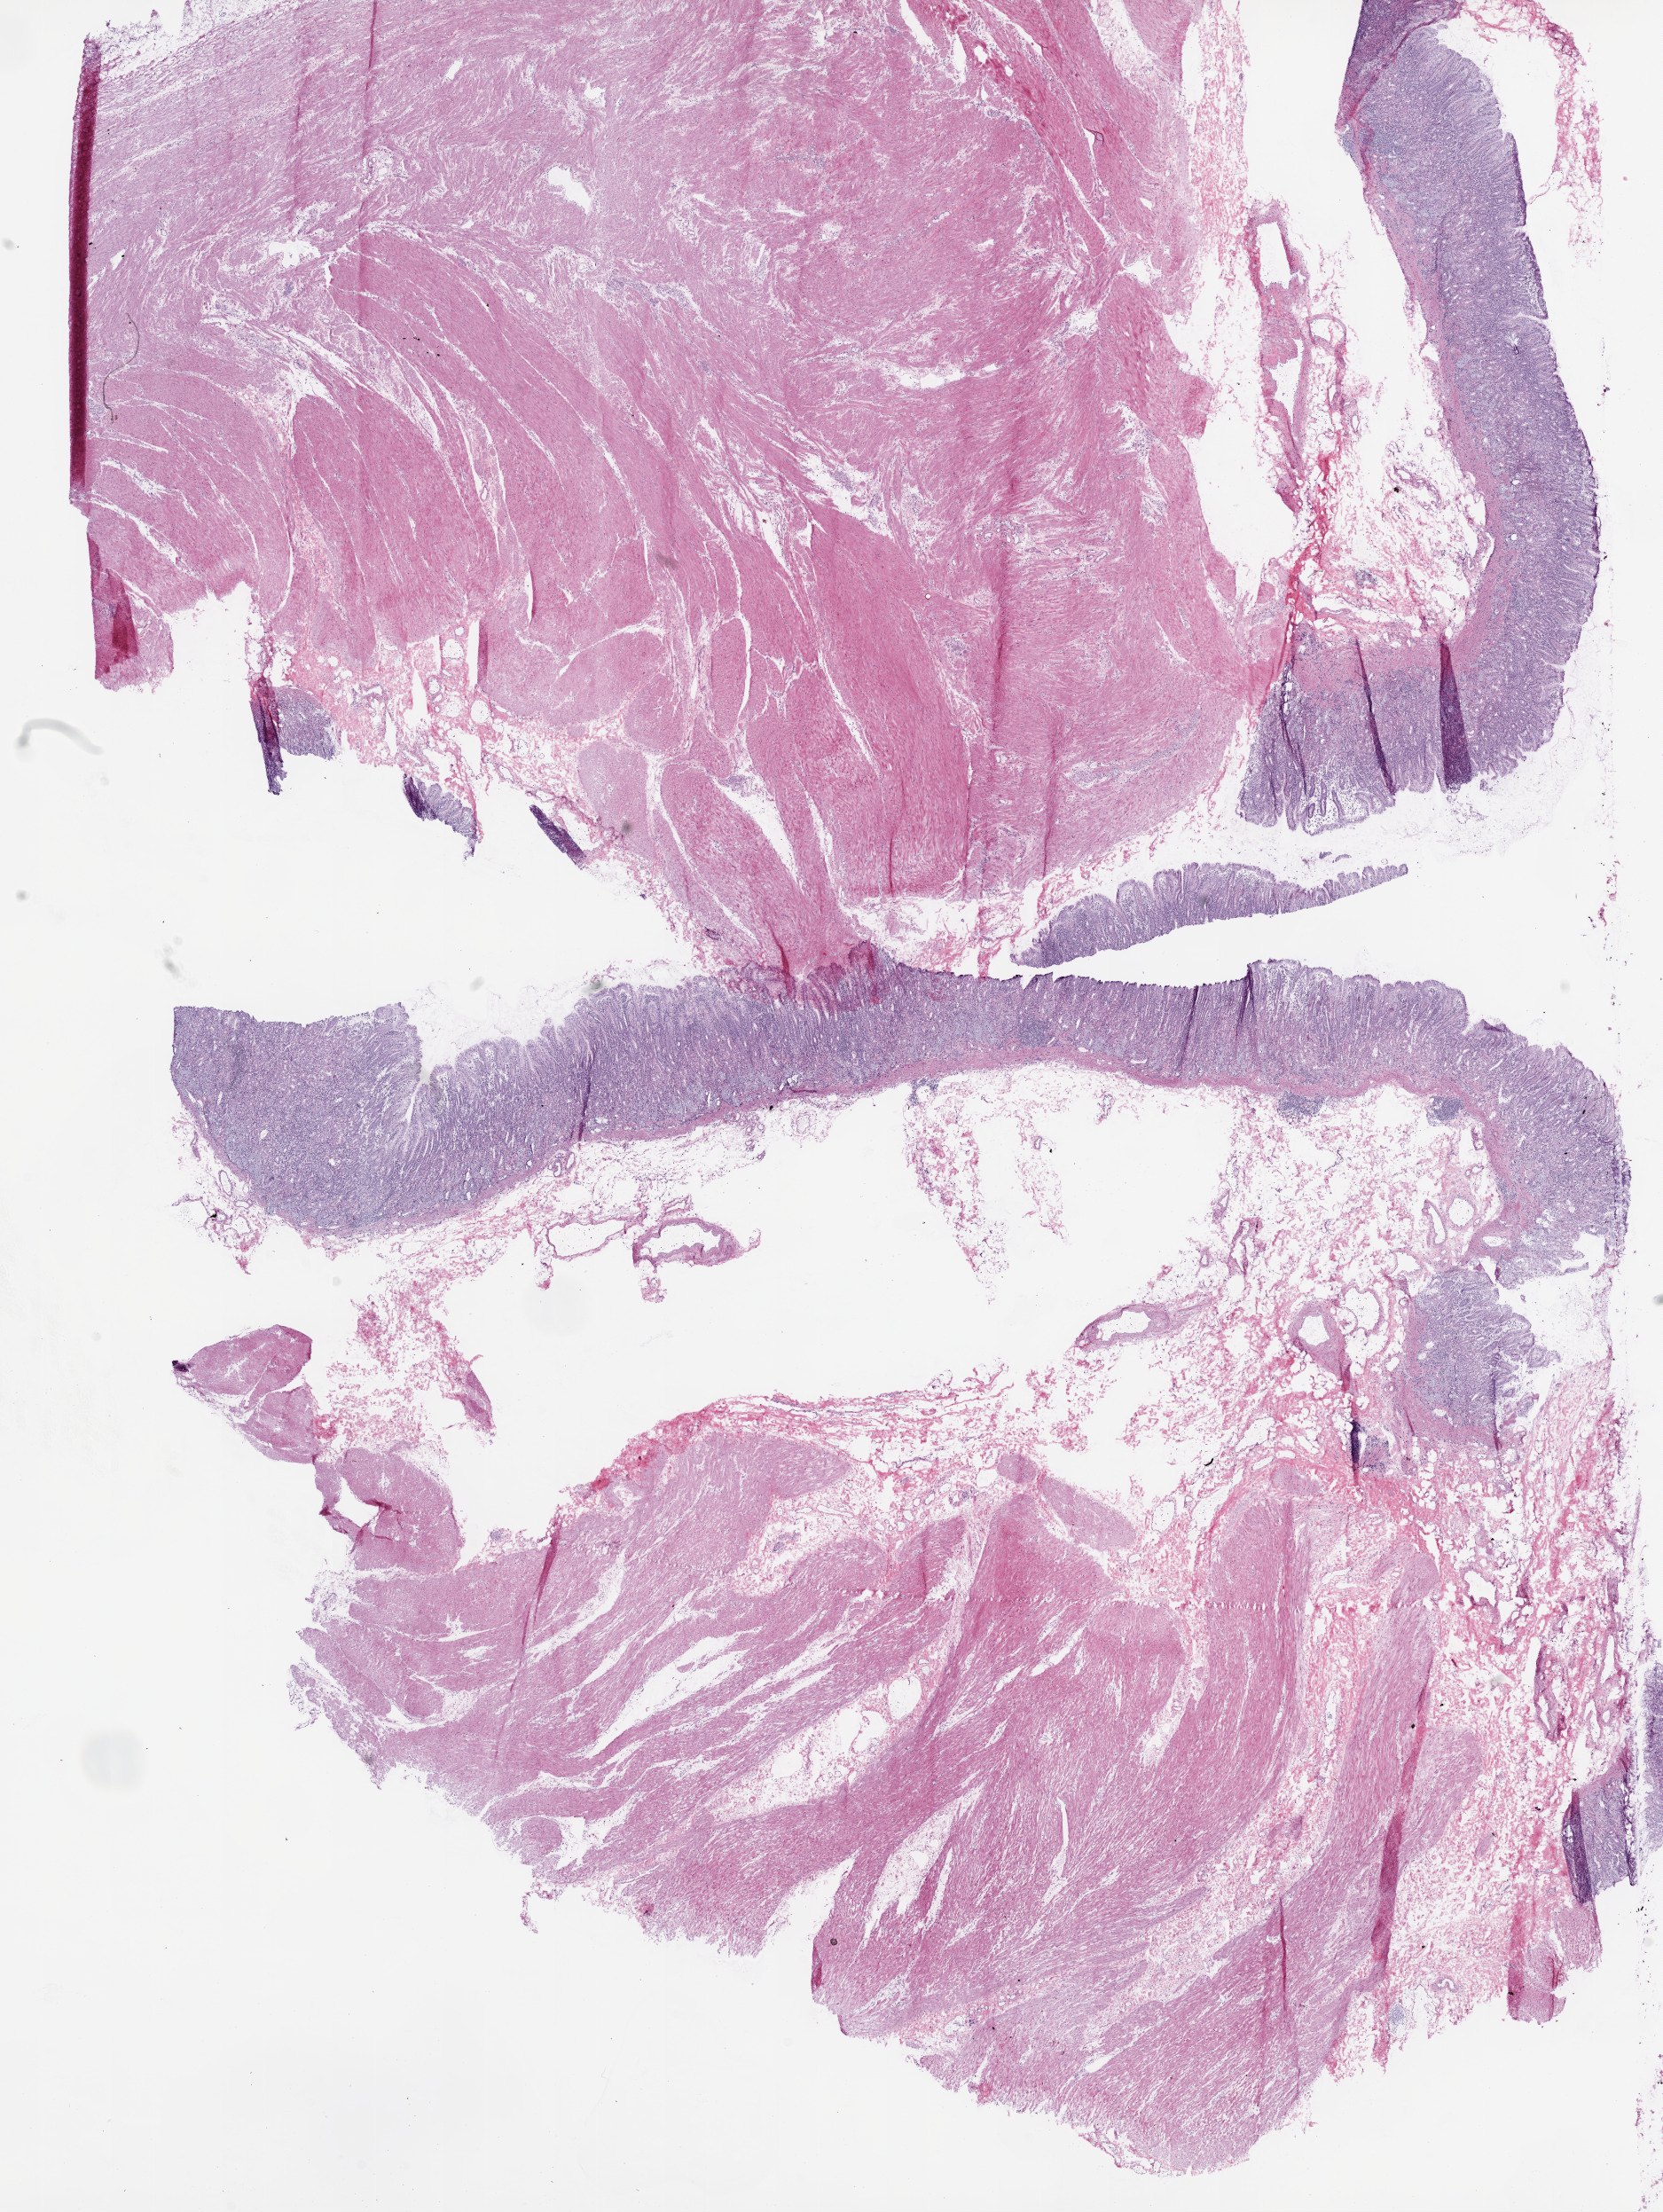
Whole-slide histology image, H&E — shown as a low-resolution overview of the whole scanned area (about 15.0 x 20.0 mm, acquisition: 20x scan), frozen section, stomach, solid tissue normal (non-tumour tissue) sample. Patient: male, age at initial diagnosis 87 years.
This section: solid tissue normal sample (biorepository sample class). Patient diagnosis: Adenocarcinoma, NOS (gastric antrum).